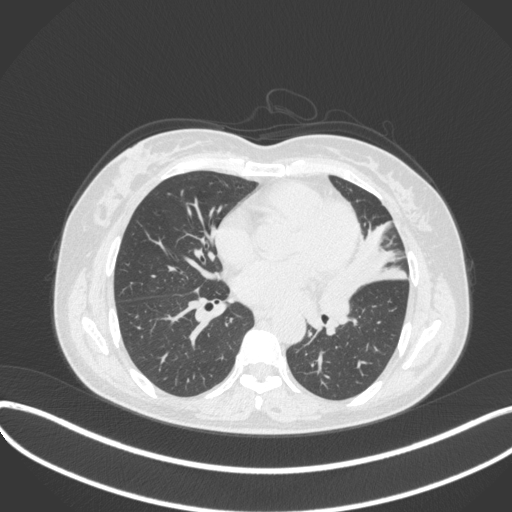
Chest CT, one axial slice. Slice 166 of 373 in the series (ordered by position). Reconstruction kernel B31f. Lung window (W 1500 / L -600 HU). 1 mm slice thickness. 512 × 512 image matrix, field of view 400 × 400 mm. Female patient, age 54 years. Case-level facts recorded for this patient, not image findings: clinical TNM (as recorded): T2a N1 M0; histopathological grade: G3.
Structures marked on this image (rectangle marked by the reading radiologist):
- lung tumour (recorded histology: small cell carcinoma): bounding box <320,271,367,332> (left, top, right, bottom; pixels)